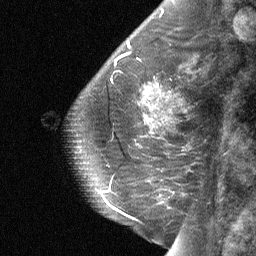
Breast MRI (dynamic contrast-enhanced), one sagittal slice. Slice 23 of 64 in the series (ordered by position). Dynamic contrast-enhanced study with each time point stored as its own series, time point 2 of 3 at this slice position (early post-contrast, ordered by acquisition time). 1.5 T. TE 4.8 ms, TR 27 ms. 2 mm slice thickness. 256 × 256 image matrix, field of view 180 × 180 mm. Patient: female, 59 years. From the clinical record (not read from this slice): setting: breast cancer imaged before/during neoadjuvant chemotherapy; receptor status: triple-negative.
Outlined on this slice (semi-automatically segmented with operator editing):
- analysis volume of interest (the breast-tissue region the enhancement analysis was run in; not a lesion): bounding box <133,75,173,114> (left, top, right, bottom; pixels)
- tumour enhancement mask (voxels above the 90 % enhancement threshold inside the analysis volume of interest): <145,84,159,100>